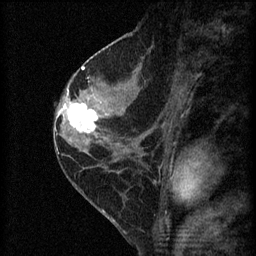
Breast MRI (dynamic contrast-enhanced), one sagittal slice; slice 31 of 60 in the series (ordered by position); 3 images stored at this slice position (order not interpretable as contrast timing); 1.5 T; TE 4.2 ms, TR 8.2 ms; 2 mm slice thickness; 256 × 256 image matrix, field of view 180 × 180 mm. Patient: female, 45 years.
Outlined on this slice (semi-automatic segmentation, software-assisted and operator-edited):
- analysis volume of interest (the breast-tissue region the enhancement analysis was run in; not a lesion): box from (x=62, y=98) to (x=104, y=139) px
- tumour enhancement mask (voxels above the 70 % enhancement threshold inside the analysis volume of interest): (x=62, y=100)–(x=99, y=133)